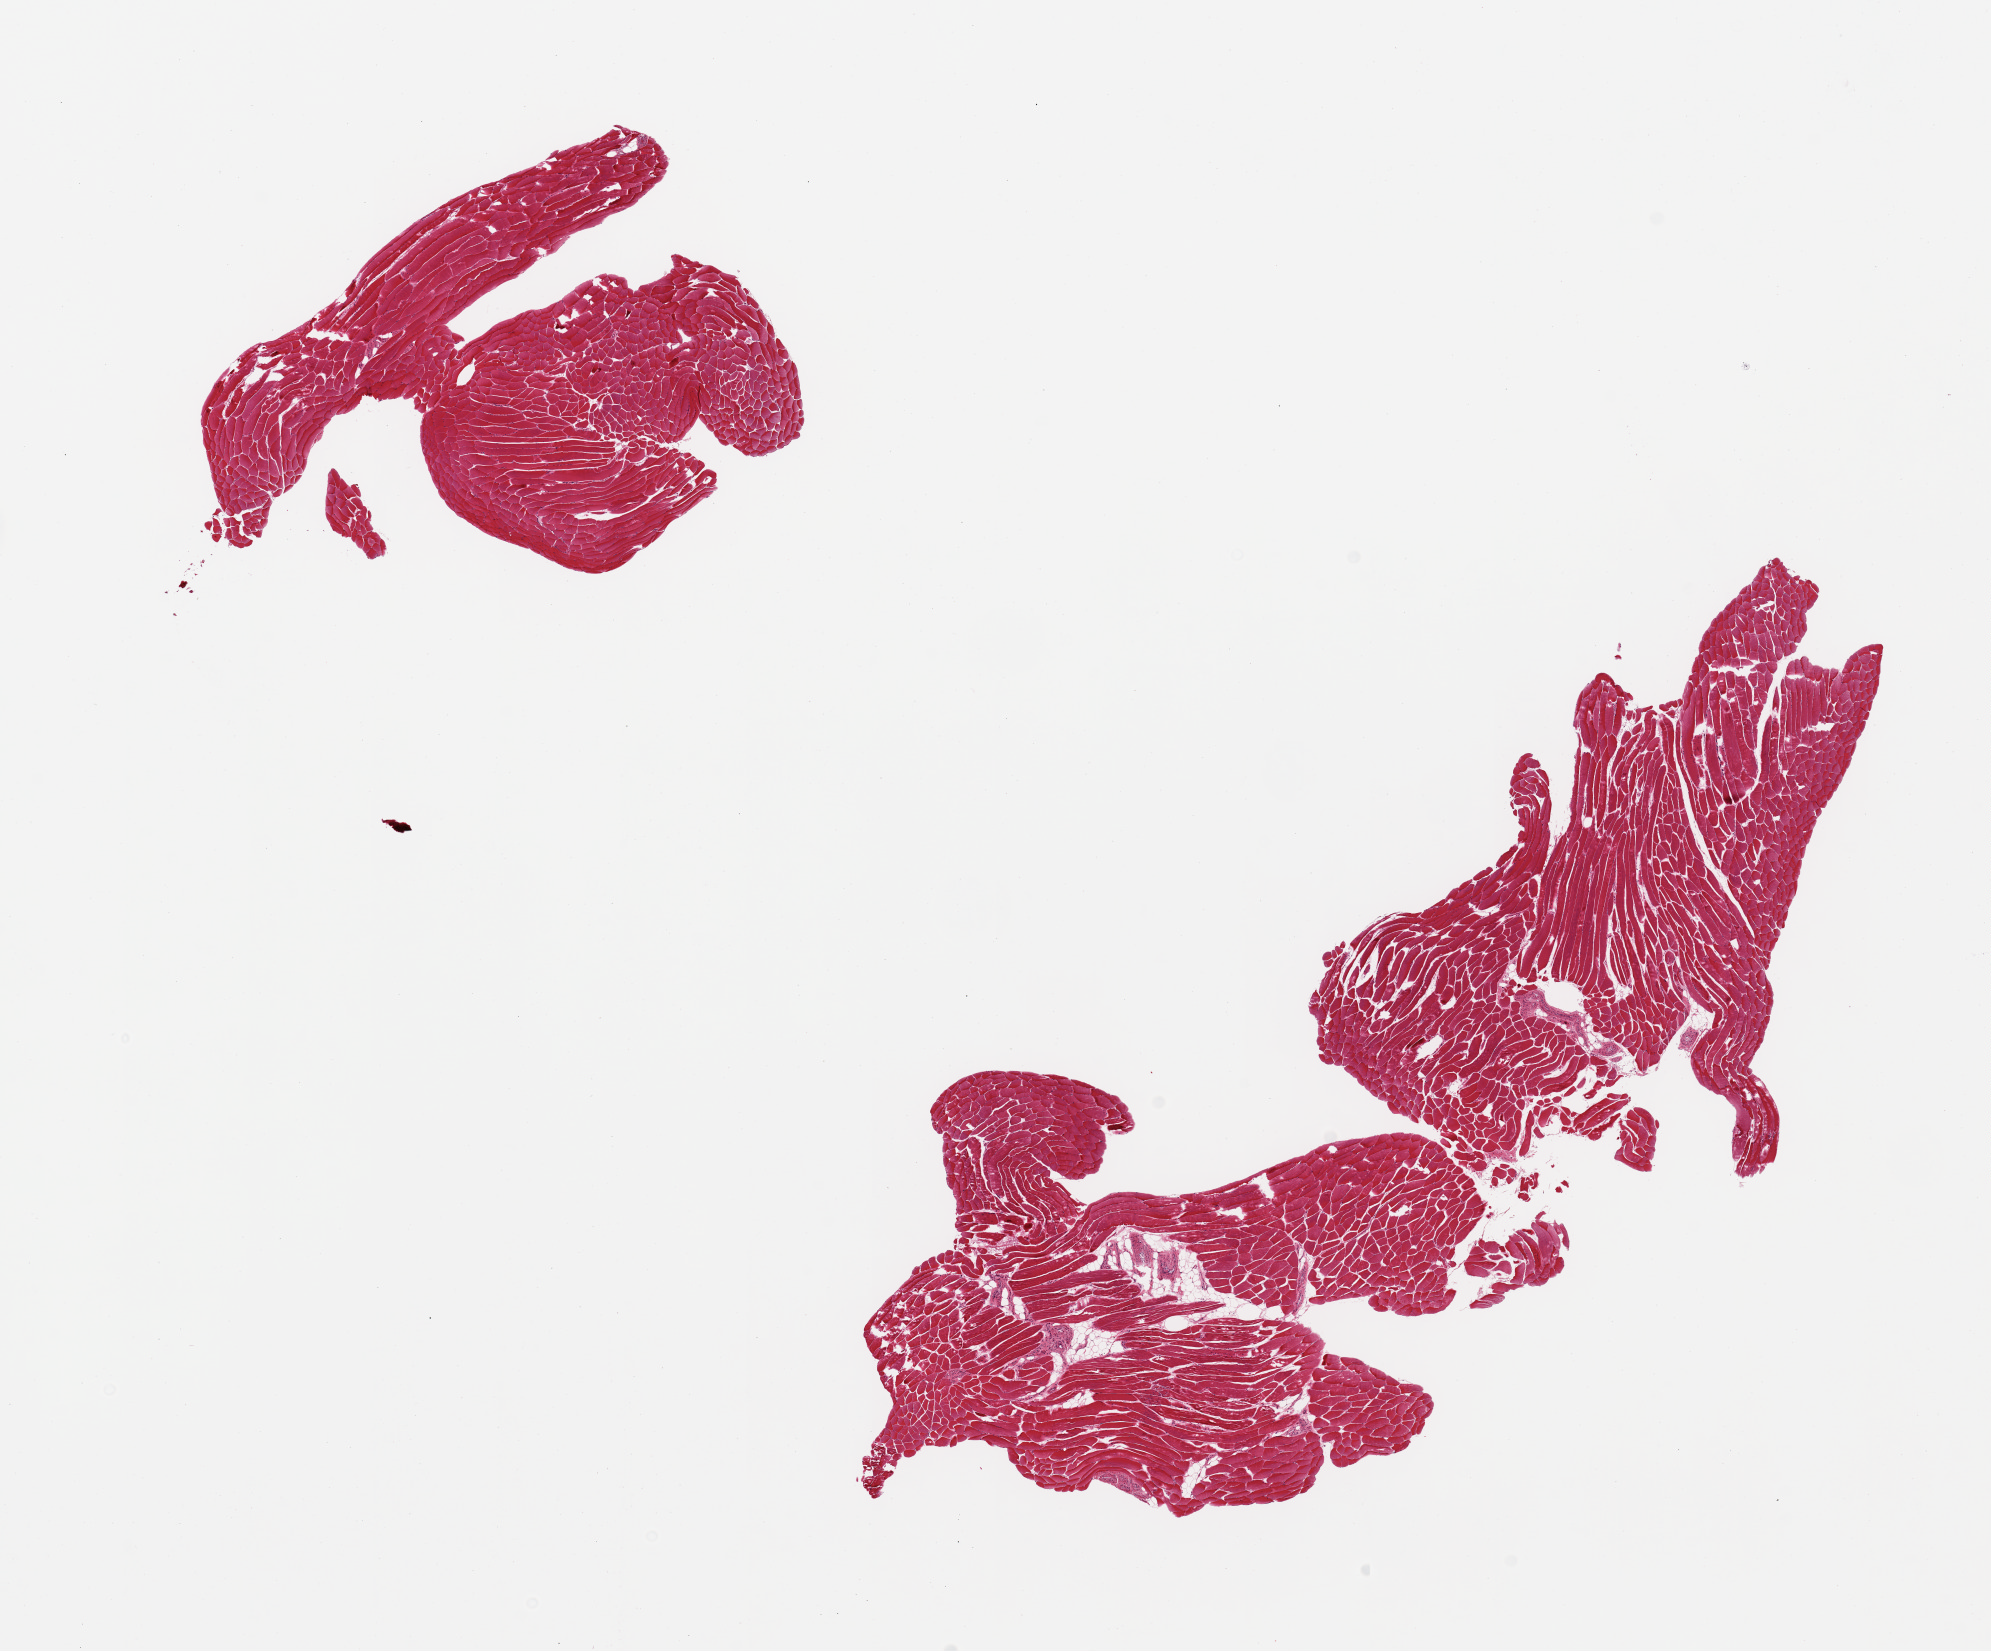
Digitized haematoxylin and eosin-stained section — whole scanned area (about 15.8 x 13.1 mm) shown as a low-resolution overview; PAXgene-fixed, paraffin-embedded tissue; sampled site (target tissue): skeletal muscle; tissue donor sample. Donor sex: male.
Pathologist's review note for this sample: 2 pieces, only trace interstitial fat; good specimens.